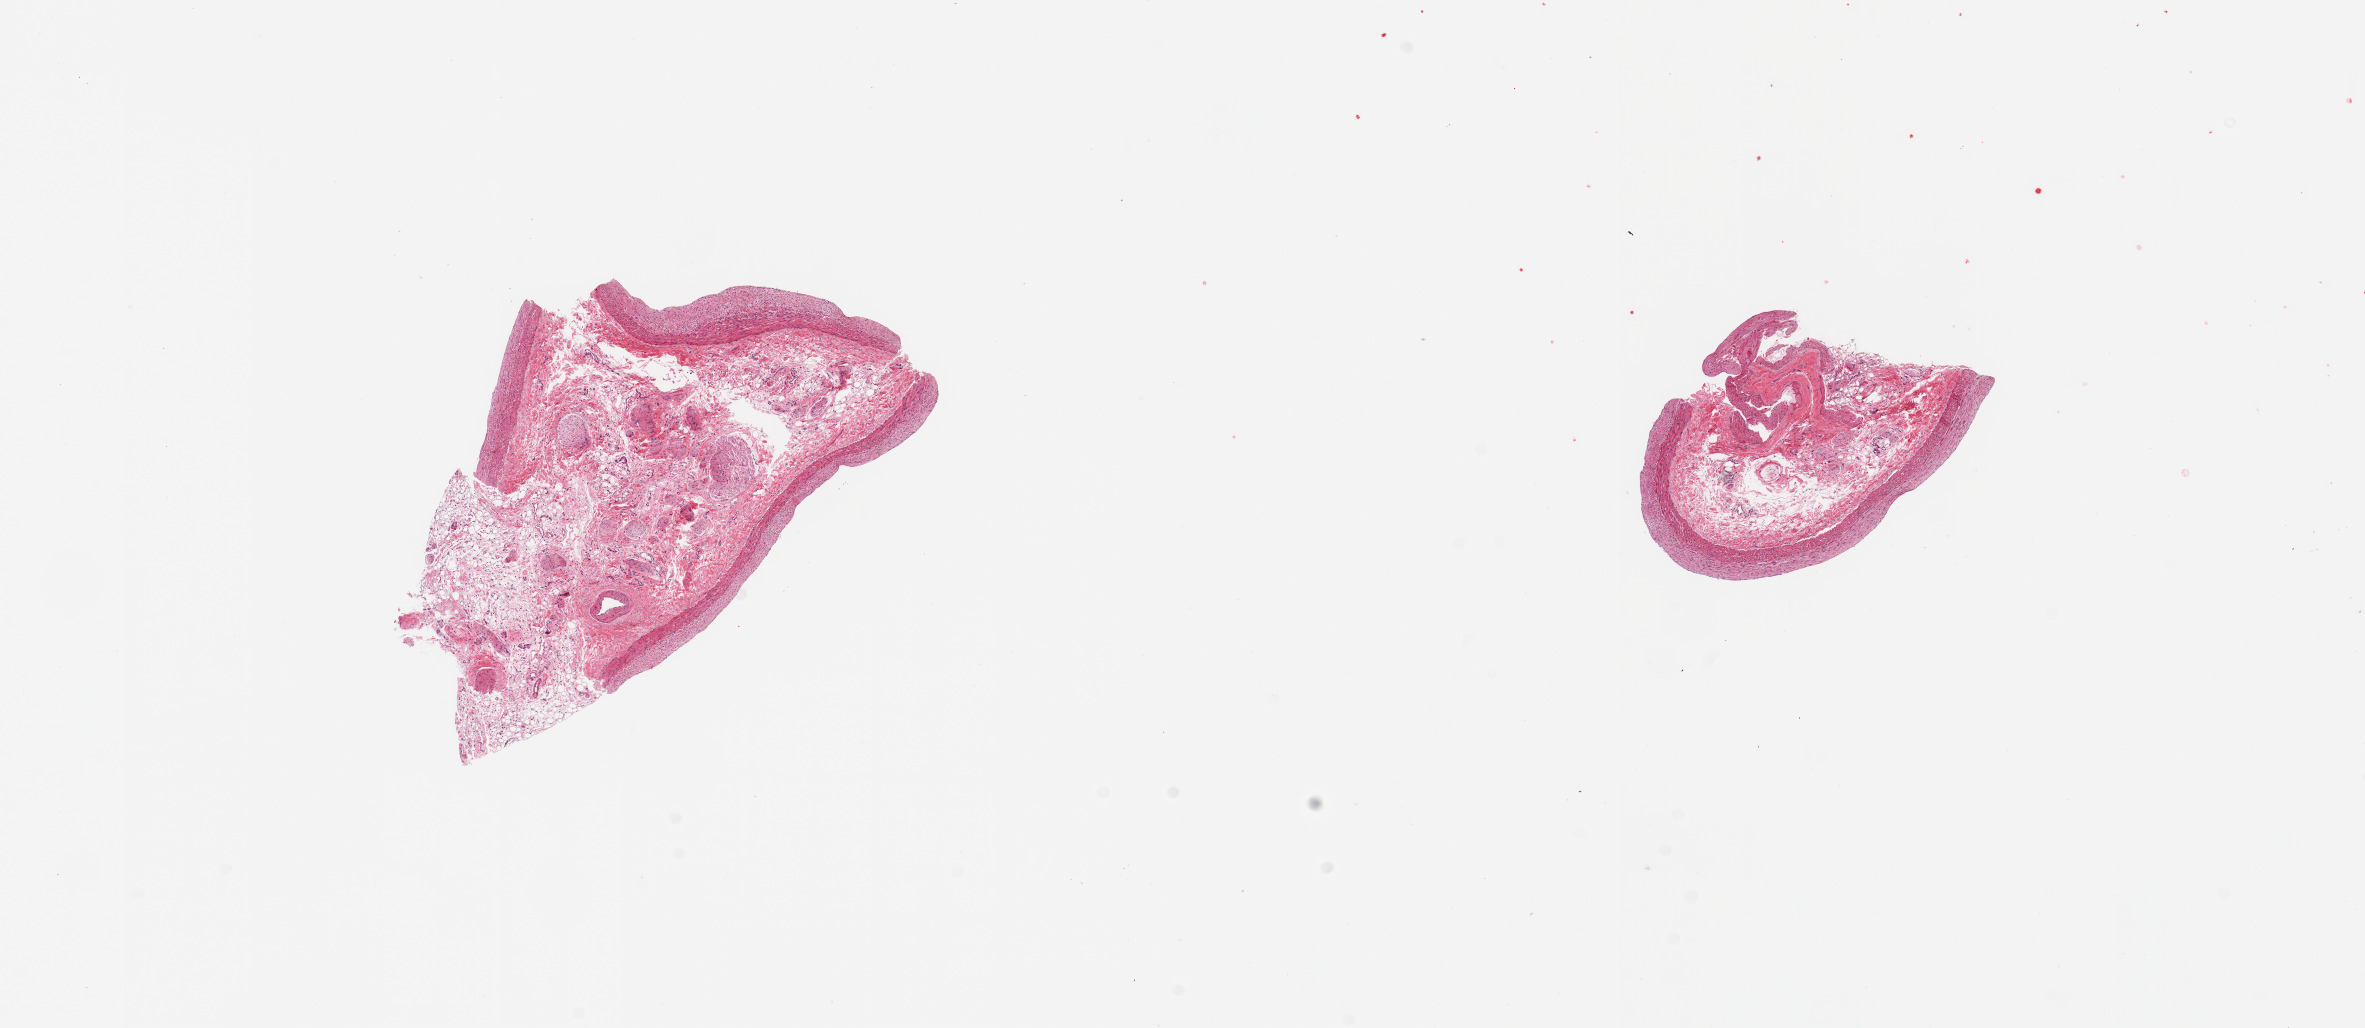
Digitized haematoxylin and eosin-stained section — whole scanned area (about 18.7 x 8.1 mm) shown as a low-resolution overview; PAXgene-fixed paraffin-embedded (PFPE) section; sampled site (target tissue): coronary artery; donor tissue sample. Donor sex: male.
• review note (as recorded): 2 pieces; >60% is fibroconnective tissue and nerve